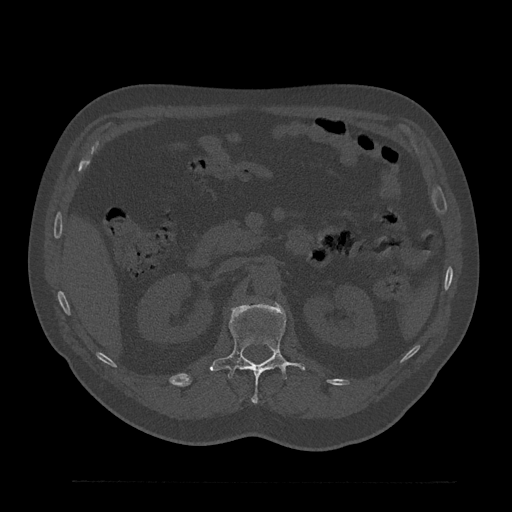
CT including the spine, one axial slice; 120 kVp; bone window (W 1800 / L 400 HU); 0.5 mm slice thickness; 512 × 512 image matrix, field of view 430 × 430 mm. Male patient, age 61 years. Case-level facts recorded for this patient, not image findings: primary cancer: prostate.
Annotated regions visible in this slice (semi-automatically segmented with operator editing):
- L1 vertebra: bounding box [x1, y1, x2, y2] px = [210, 302, 305, 403]